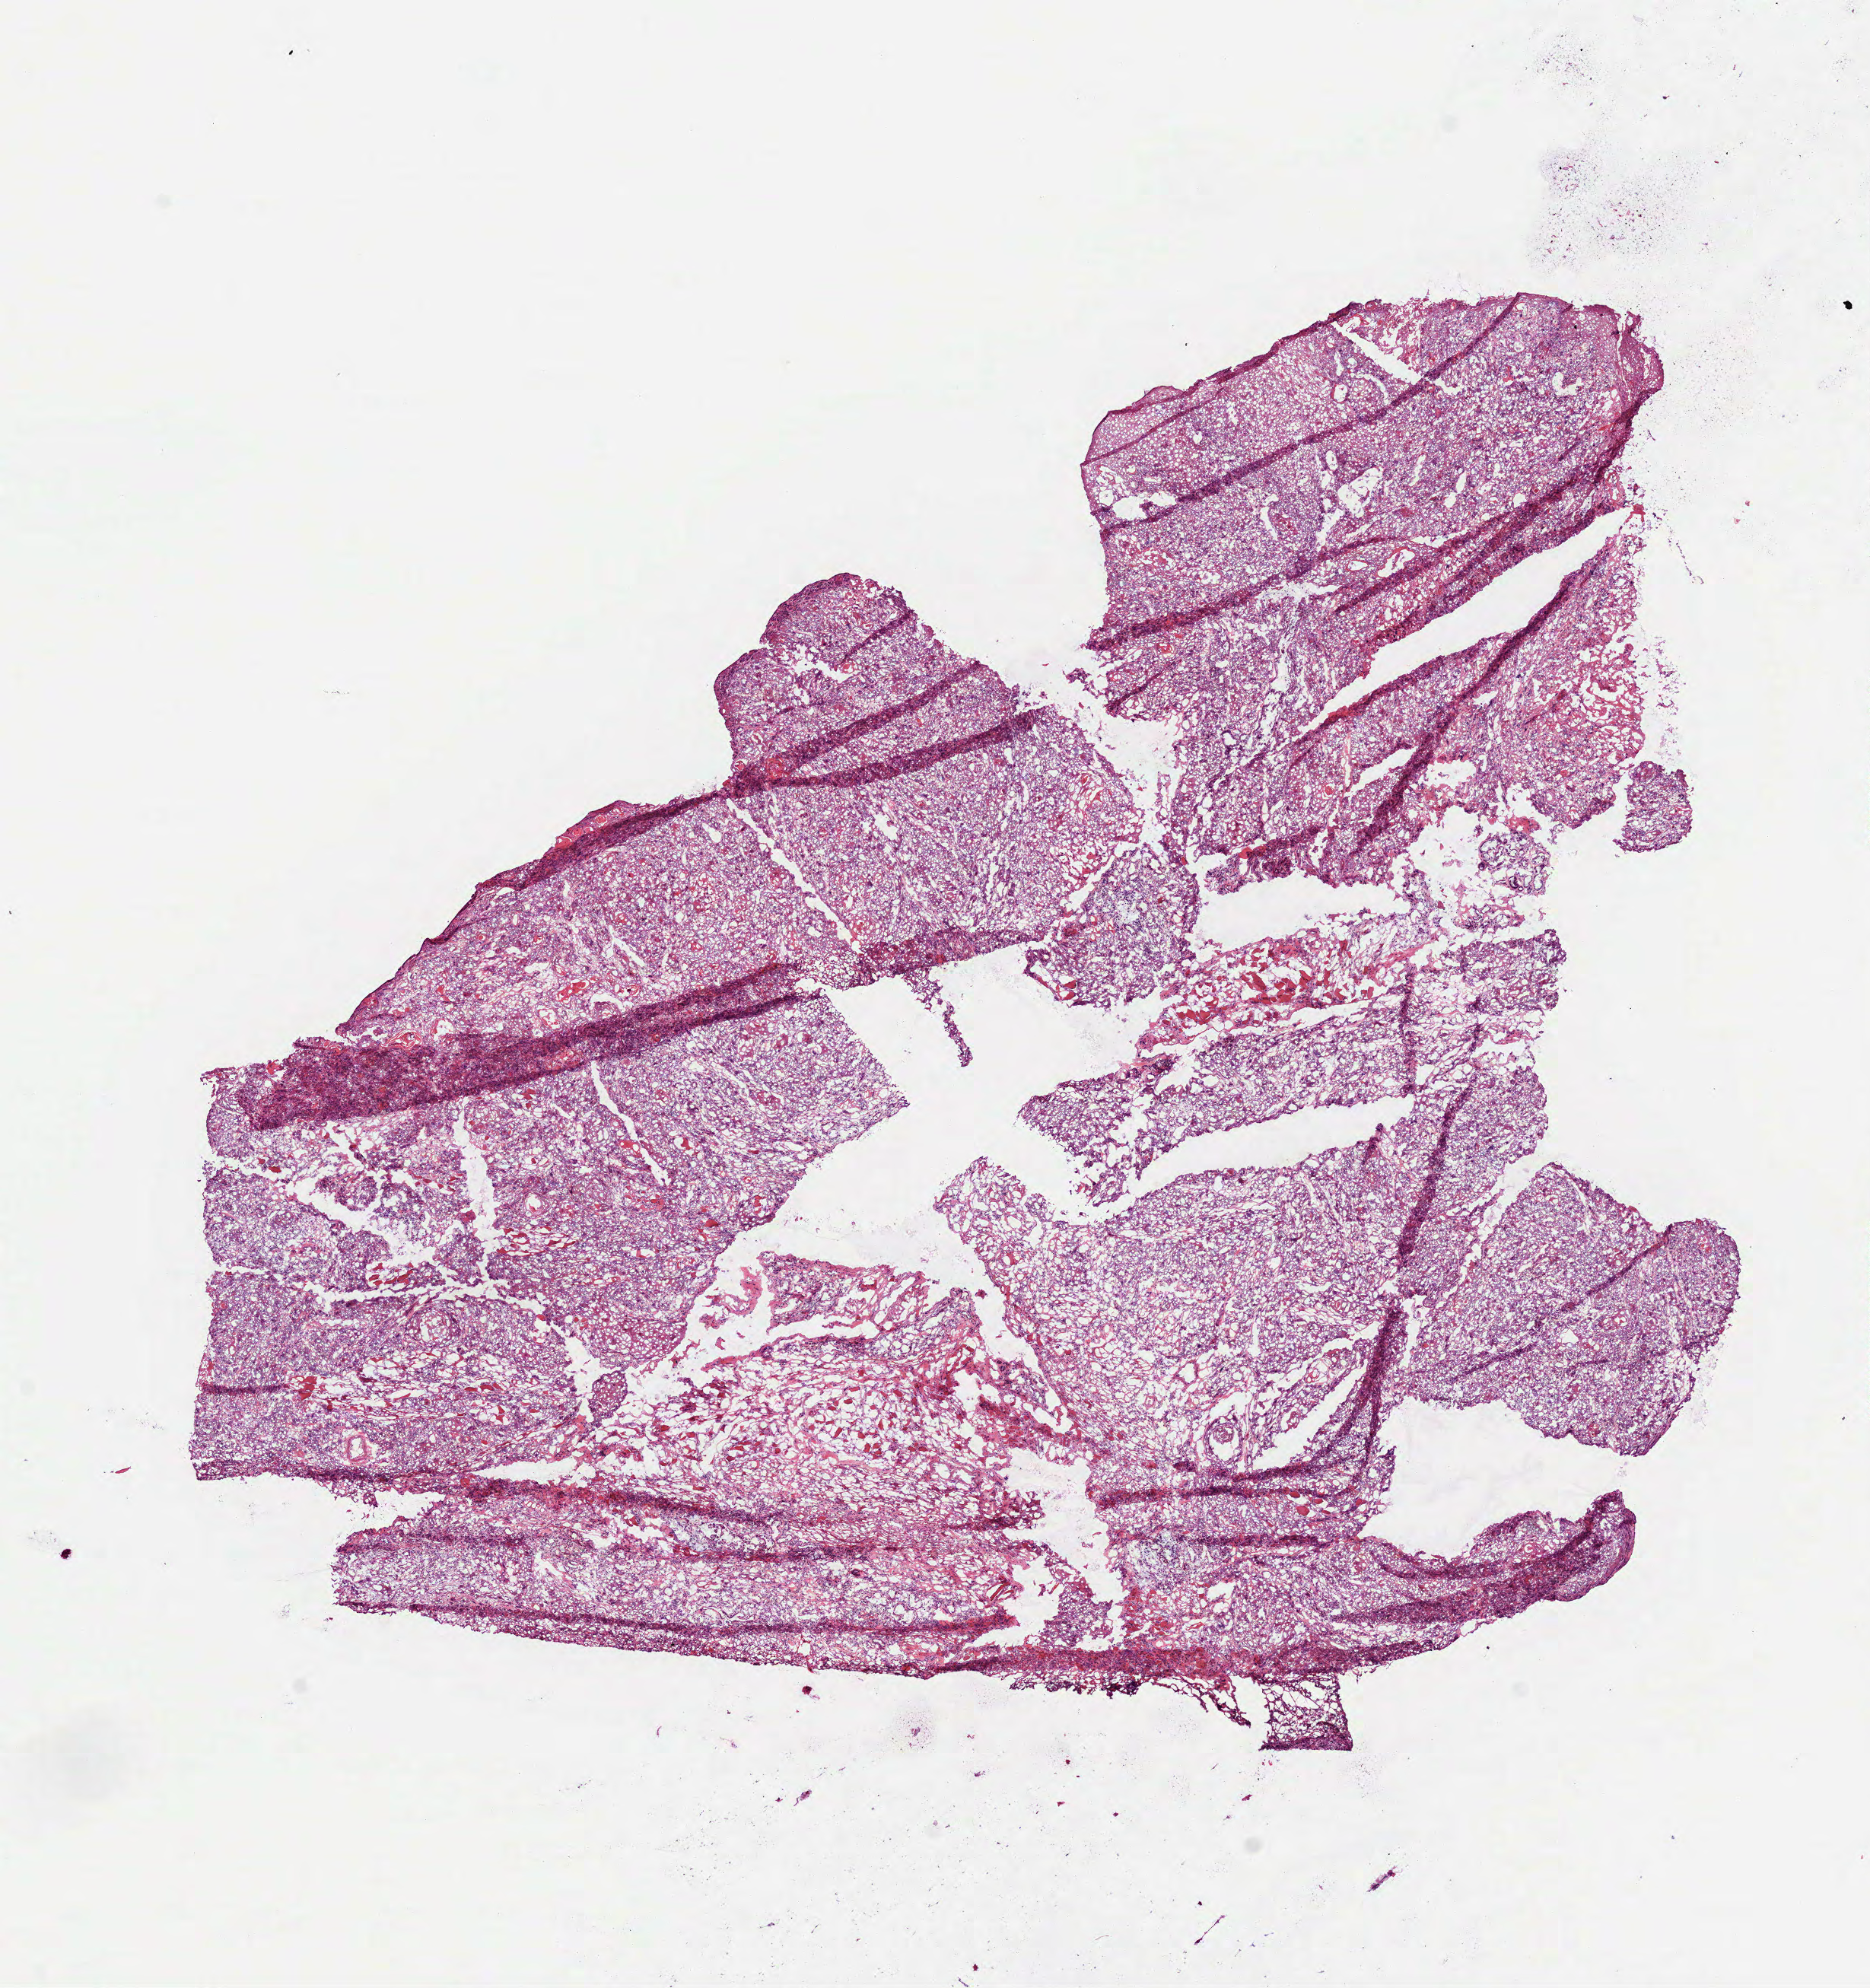
Digitized H&E tissue section (whole slide), a low-resolution overview of the entire scanned area, about 9.9 x 10.5 mm (slide scanned at 40x); frozen section from the bottom of the tissue portion; head and neck, primary tumour sample. Patient: female, age at initial diagnosis 32 years. Slide review estimates, as recorded: tumour cells 85%, tumour nuclei 85%.
Pathologic diagnosis: Squamous cell carcinoma, NOS (tongue, NOS).